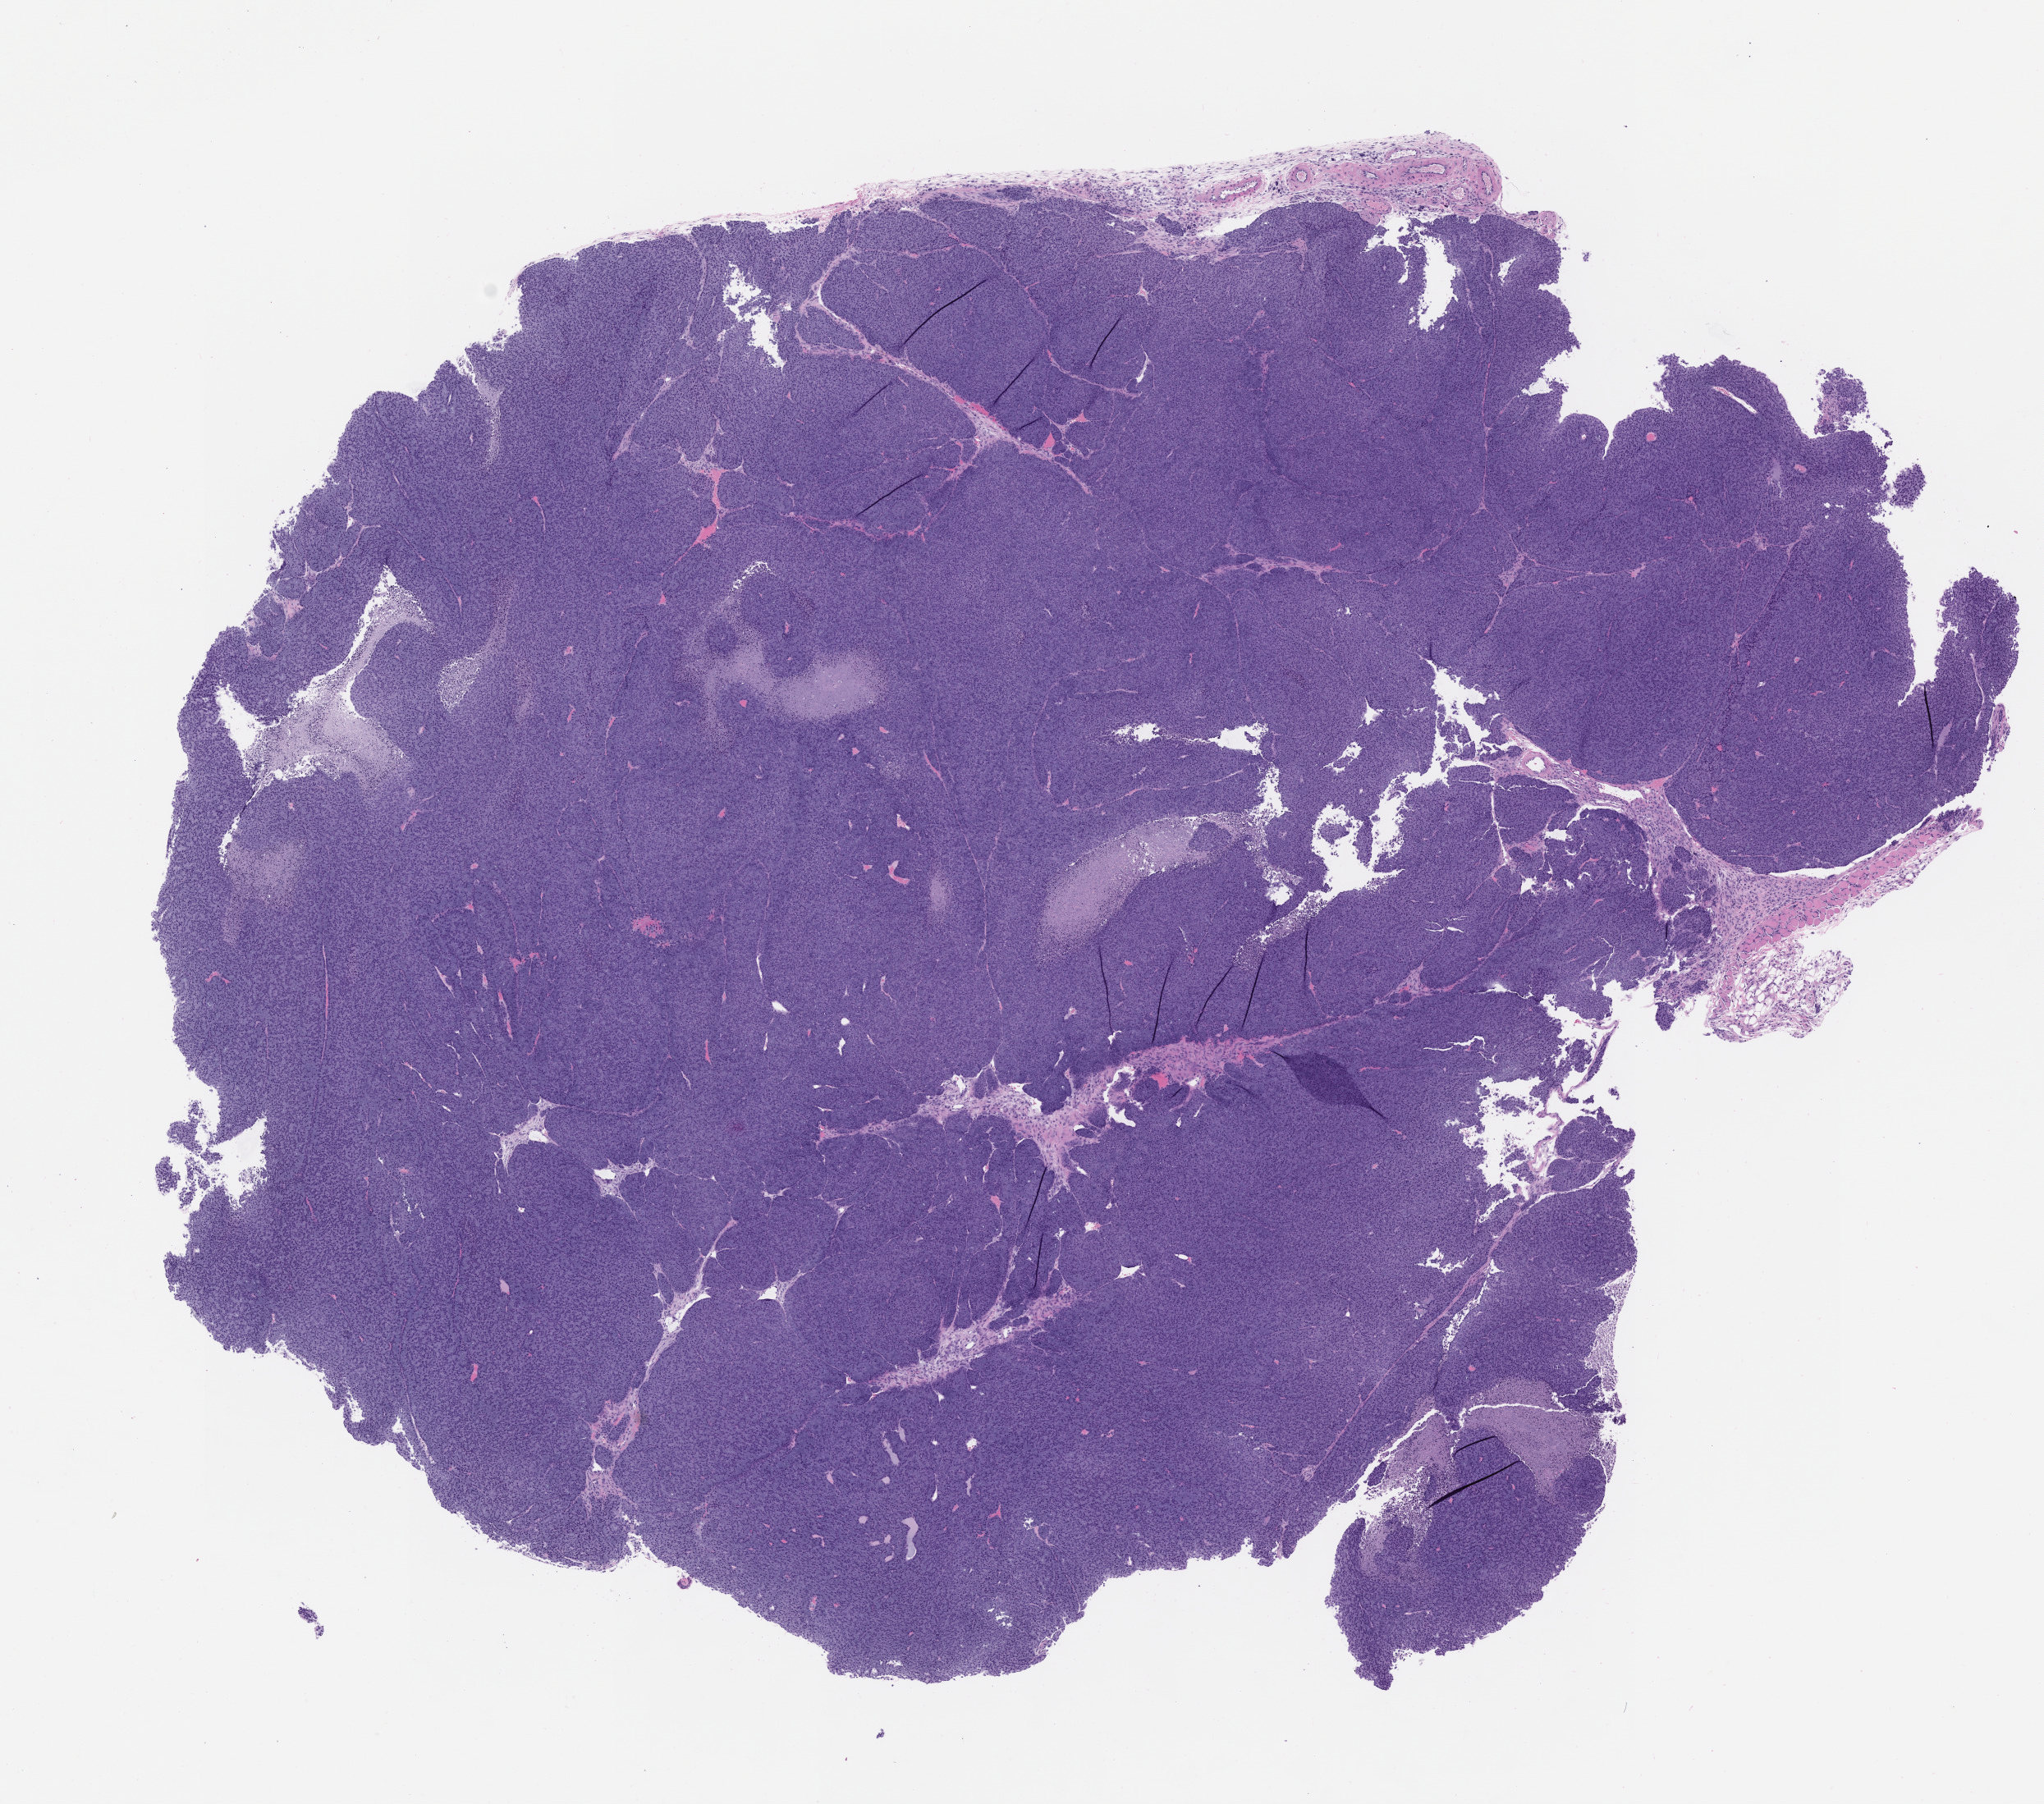
Whole-slide image, hematoxylin and eosin (H&E): patient-derived xenograft (human tumor grown in a mouse), passage 2 — shown as a low-resolution overview of the whole scanned area (about 10.0 x 8.8 mm); FFPE section; originating tumor site category: head and neck.
Originating patient diagnosis: Acinar Cell Carcinoma.